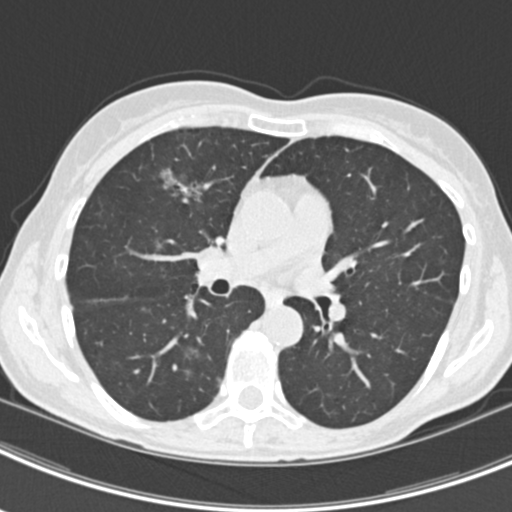
Chest CT (low-dose screening protocol), one axial image; second screening round (one year after baseline); lung window (W 1500 / L -600 HU); 2 mm slice thickness. Female participant, aged 63 years at enrolment. Current smoker at enrolment.
Expert-annotated lung lesion, bounding box [x1, y1, x2, y2] px = [158, 158, 218, 211]. The screening reader recorded 9 non-calcified nodules or masses ≥4 mm on this exam (left upper lobe, right upper lobe, left upper lobe, left lower lobe, right middle lobe, left lower lobe, left lower lobe, right lower lobe, right lower lobe); which of them this box marks is not recorded. Official screen result: positive, other. Later outcome: lung cancer diagnosed 408 days after this screen (after the third annual screen) — bronchiolo-alveolar adenocarcinoma, NOS, right upper lobe, right middle lobe, right lower lobe, left upper lobe, left lower lobe, moderately differentiated (G2), stage IV (AJCC 6th edition).